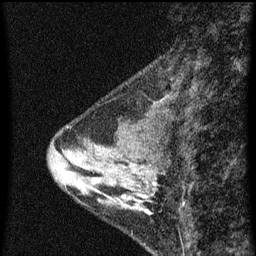
Breast MRI (dynamic contrast-enhanced), one sagittal slice; slice 22 of 60 in the series (ordered by position); dynamic contrast-enhanced series, image 2 of 3 at this slice position (ordered by acquisition); 1.5 T; TE 4.2 ms, TR 8 ms; 2 mm slice thickness; 256 × 256 image matrix, field of view 180 × 180 mm. Patient: female, 34 years.
Outlined on this slice (semi-automatic segmentation, software-assisted and operator-edited):
- analysis volume of interest (the breast-tissue region the enhancement analysis was run in; not a lesion): bounding box <70,138,159,213> (left, top, right, bottom; pixels)
- tumour enhancement mask (voxels above the 70 % enhancement threshold inside the analysis volume of interest): <122,196,147,203>